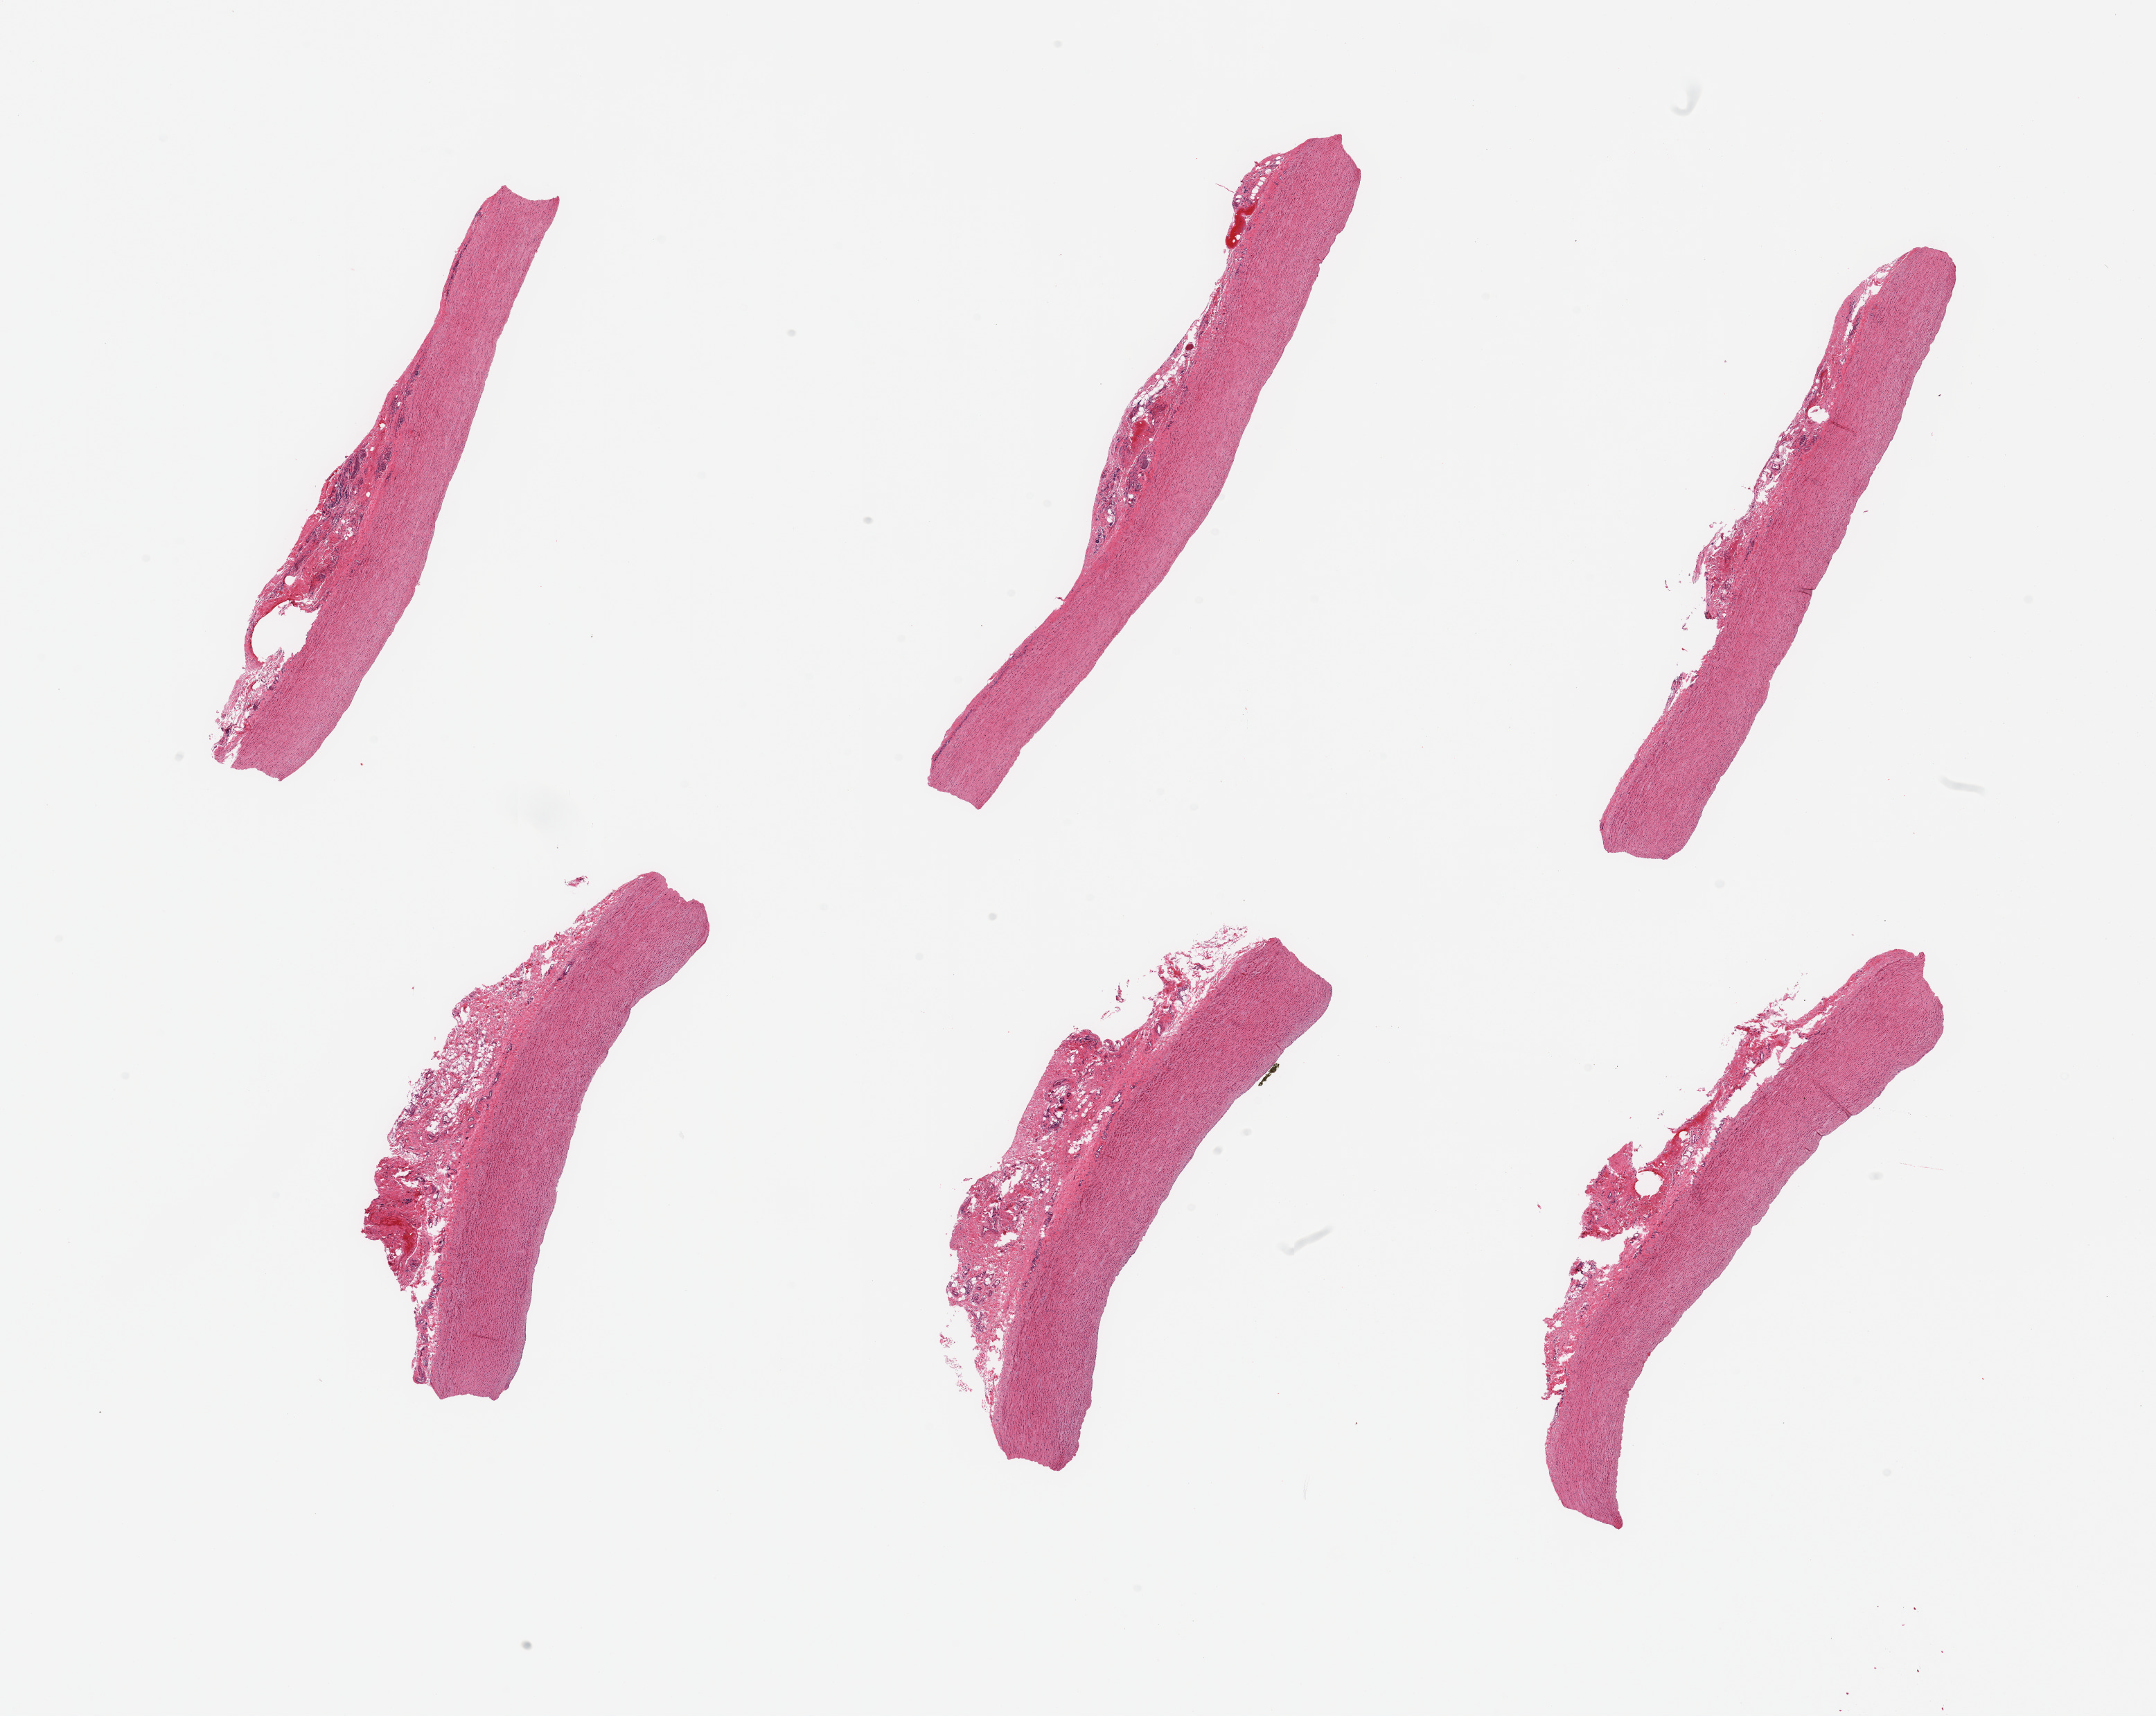
Digitized hematoxylin and eosin (H&E)-stained section — whole scanned area (about 24.6 x 19.6 mm, from a 20x scan) shown as a low-resolution overview. PAXgene-fixed, paraffin-embedded tissue. Target tissue: aorta. Tissue donor sample. Female donor.
• review note (as recorded): 6 pieces; no intimal lesions; up to 0.9mm thickfibrovascular adventitia